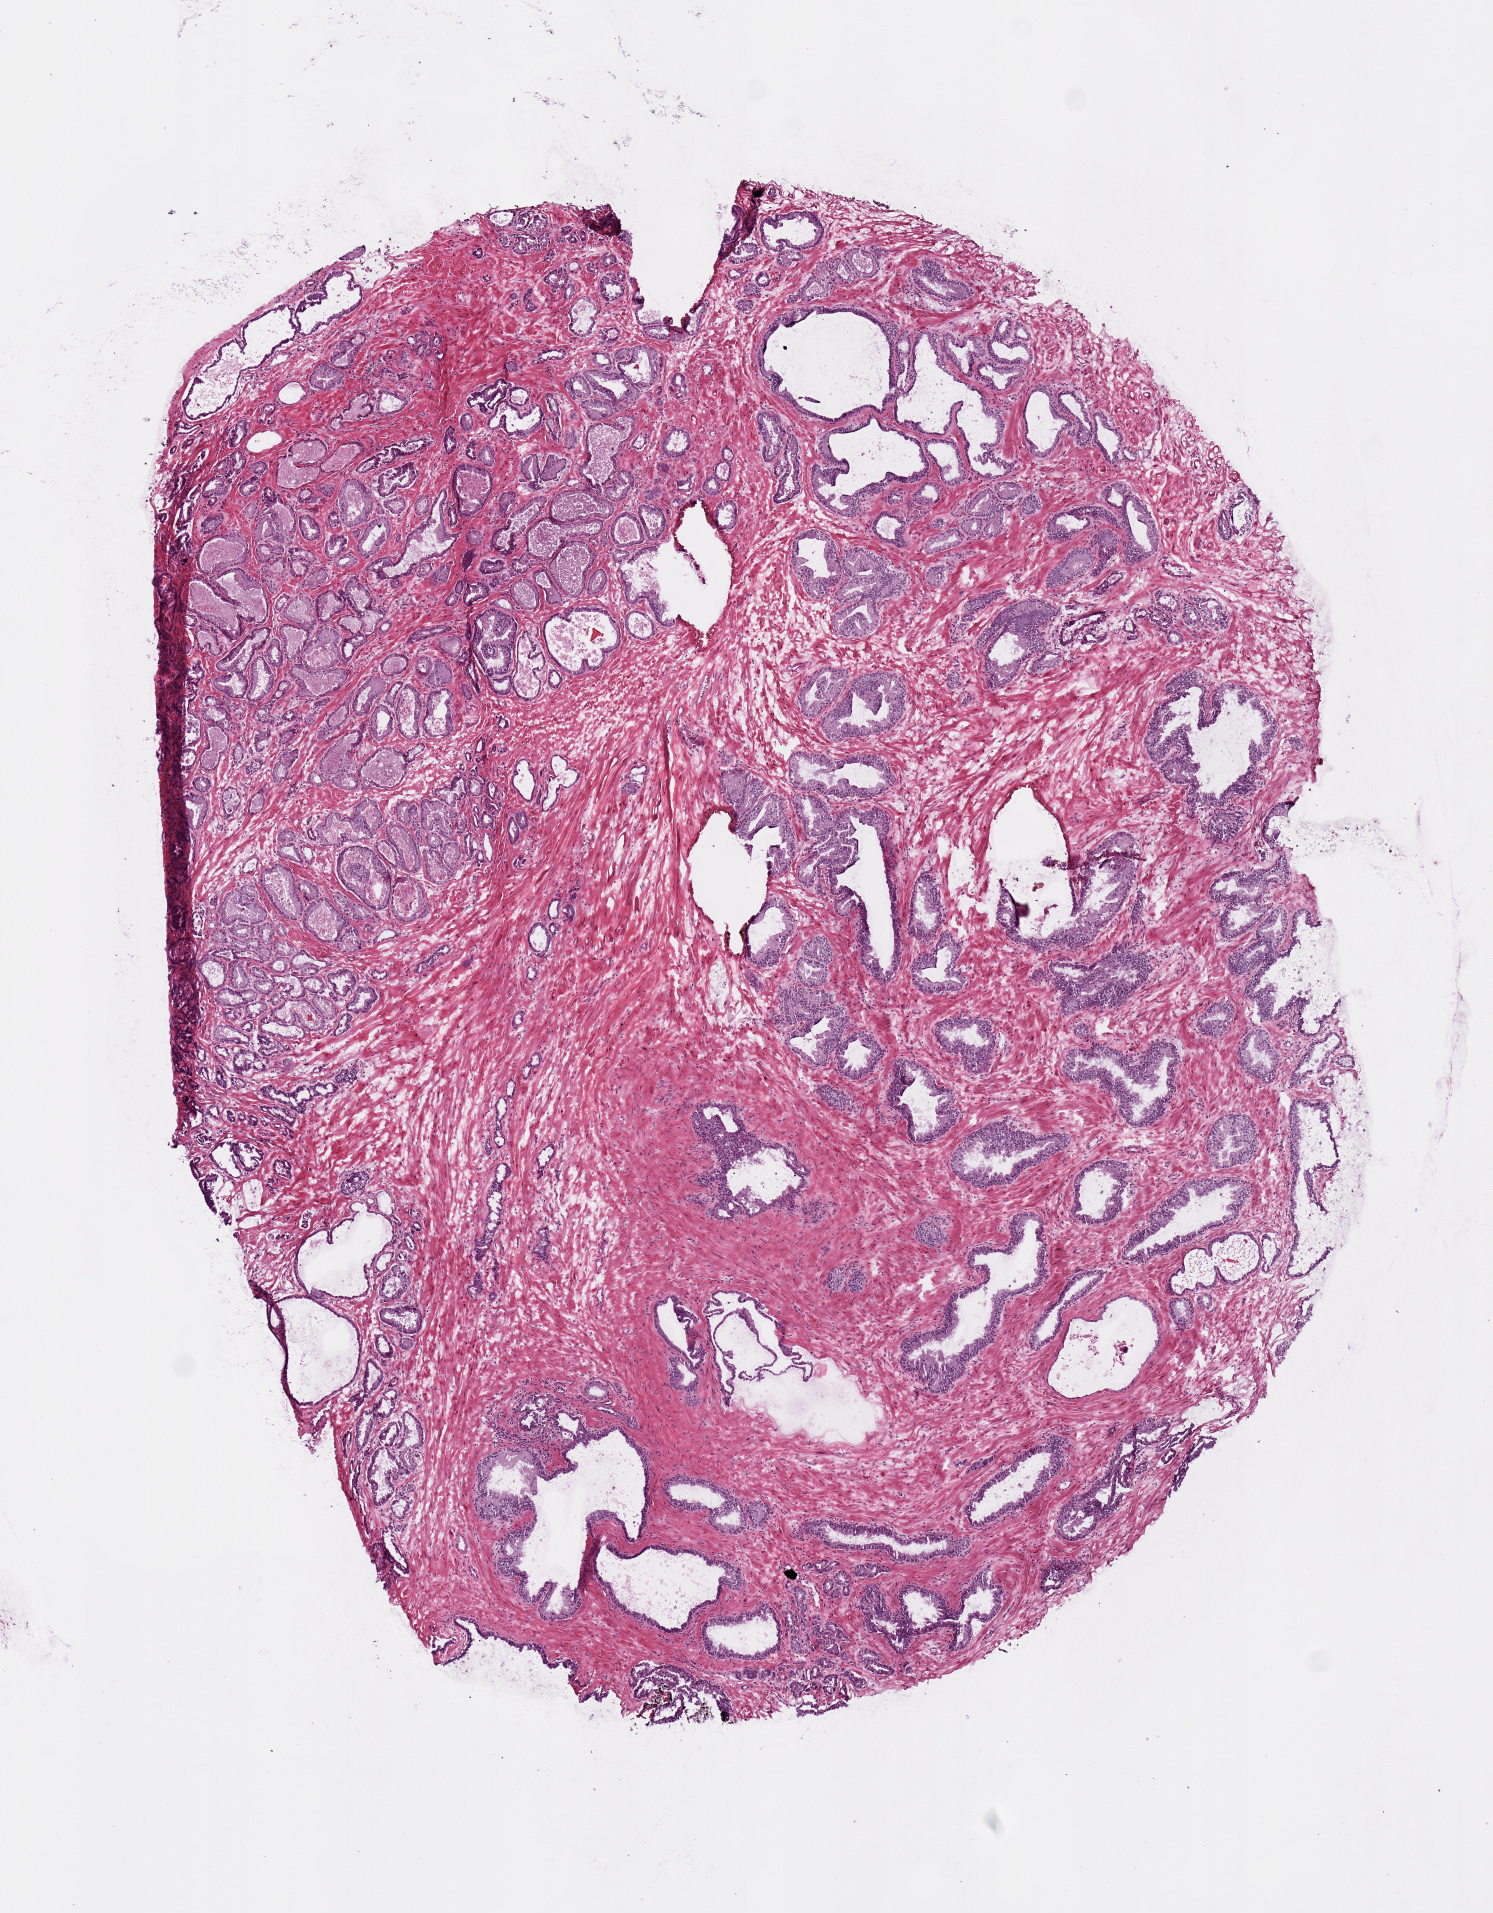
Digitized H&E tissue section (whole slide) — whole scanned area (about 5.9 x 7.6 mm) shown as a low-resolution overview. Frozen section from the top of the tissue portion. Sample: primary tumour, prostate. Male patient; age at initial diagnosis 50 years. Gleason score: 7 (3+4). Pathologist review of this section (percent, as recorded): tumour cells 70%, tumour nuclei 70%, normal cells 10%, stromal cells 20%, necrosis 0%.
Laterality: left. Diagnosis: Acinar cell carcinoma (prostate gland).